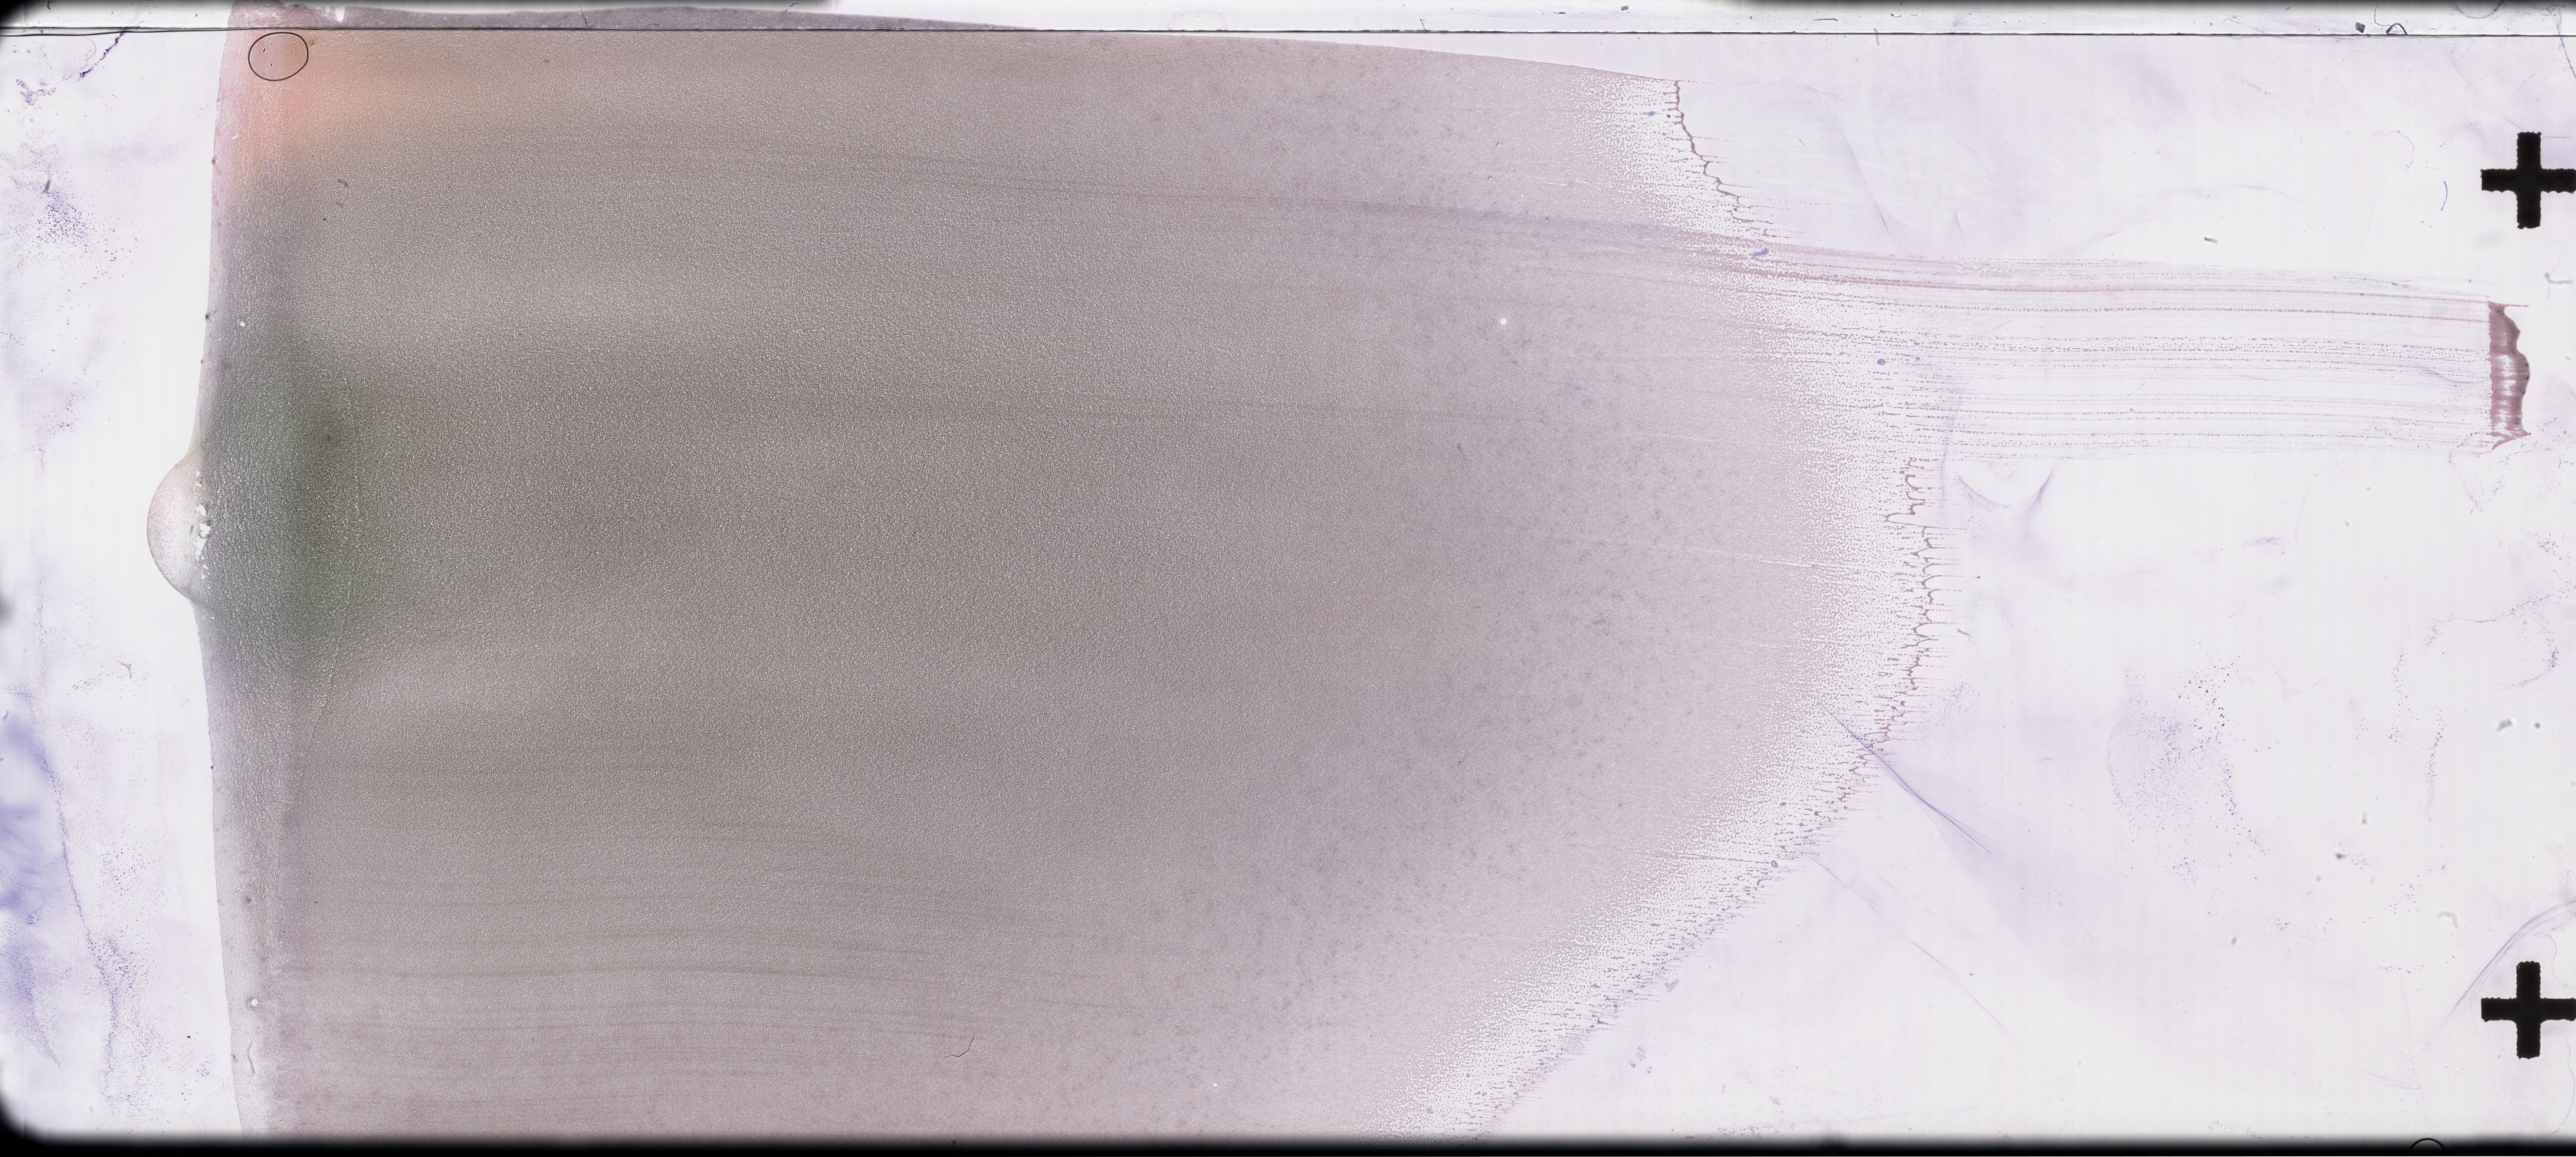
Wright–Giemsa-stained whole blood smear, whole-slide image — low-resolution overview of the scanned area, about 54.3 x 24.4 mm, specimen time point: collected on treatment. Male patient.
* from a patient with: Plasma Cell Myeloma